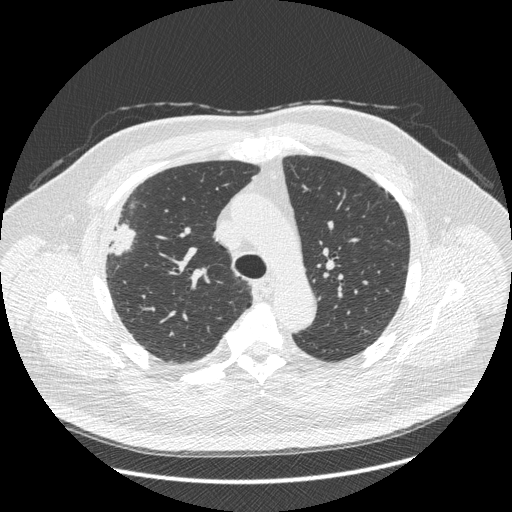
Low-dose screening chest CT, axial slice, third screening round (two years after baseline), lung window (W 1500 / L -600 HU), 1.25 mm slice thickness, standard (soft-tissue) reconstruction kernel (STANDARD), slice 122 of 426 in the series, 512 × 512 image matrix. Male, age 66 years at enrolment.
- Lesion marked by an expert reader, bounding box <87,204,147,270> (left, top, right, bottom; pixels).
- The exam's reader record, not a measurement of the box and not confirmed to be the same lesion: non-calcified nodule or mass ≥4 mm, right upper lobe, 48 × 25 mm, spiculated (stellate) margins, soft tissue attenuation, pre-existing on the prior screen: no.
- Lung cancer was diagnosed 35 days after this screen: non-small cell carcinoma, right upper lobe, stage IV (AJCC 6th edition), 50 mm at pathology.